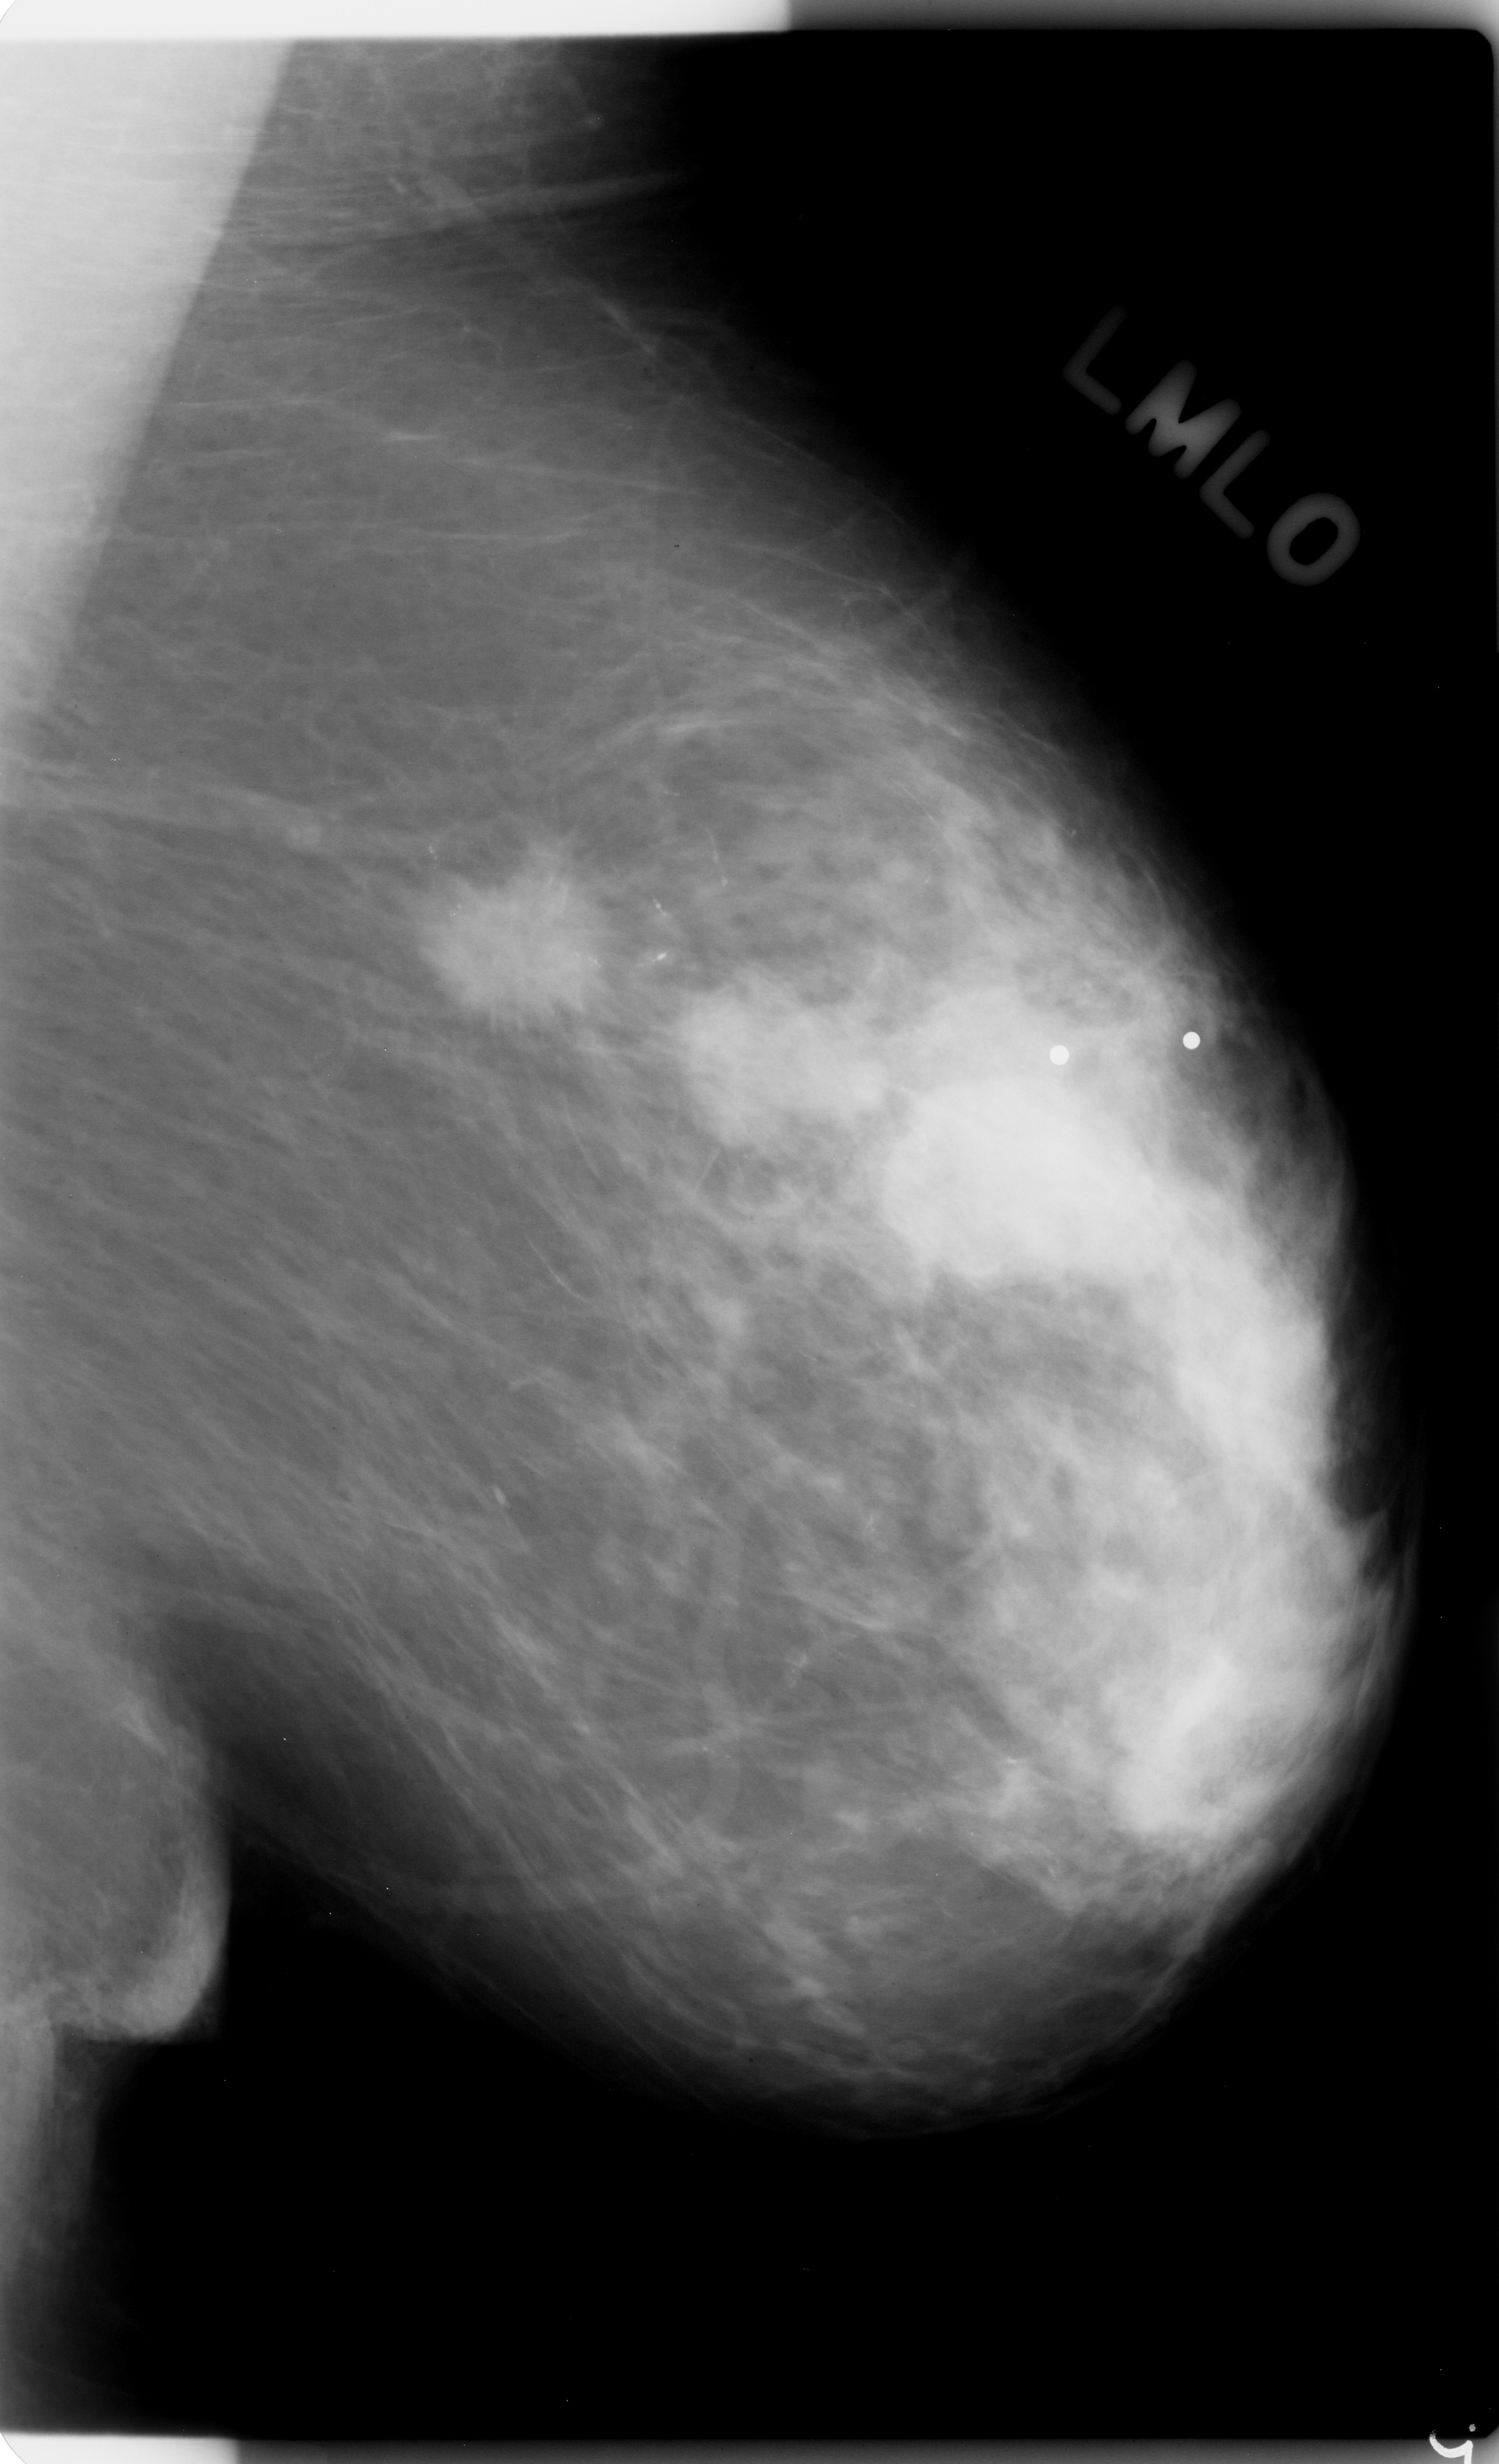
Digitized screen-film mammogram. Left breast. Mediolateral oblique (MLO) view. BI-RADS breast density category 2 (scale 1–4). 1499 × 2464 image matrix.
Expert-marked regions of interest on this image (one box per marked abnormality):
- Finding 1 of 3: mass, shape irregular, margins spiculated; BI-RADS assessment category 5; subtlety rating 5 on a 1 (subtle) to 5 (obvious) scale; pathology (as recorded): malignant: bounding box <333,828,706,1068> (left, top, right, bottom; pixels)
- Finding 2 of 3: mass, shape irregular, margins spiculated; BI-RADS assessment category 5; subtlety rating 5 on a 1 (subtle) to 5 (obvious) scale; pathology result (as recorded, not read from the image): malignant: <591,946,967,1185>
- Finding 3 of 3: mass, shape irregular, margins spiculated; BI-RADS assessment category 5; pathology result (as recorded, not read from the image): malignant: <837,1028,1260,1300>